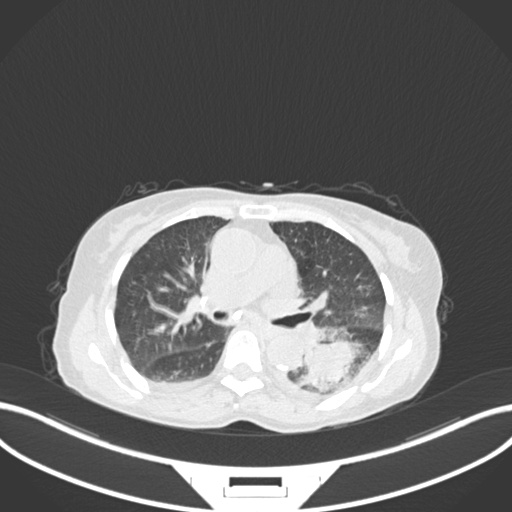
Chest CT, one axial slice; position 101 of 233 along the scan axis; reconstruction kernel B30f; lung window (W 1500 / L -600 HU); 512 × 512 image matrix. Patient: female, 78 years. Case-level facts recorded for this patient, not image findings: clinical TNM (as recorded): T3 N0 M1.
Outlined on this slice (rectangle marked by the reading radiologist):
- lung tumour (recorded histology: squamous cell carcinoma): bounding box <298,337,373,393> (left, top, right, bottom; pixels)